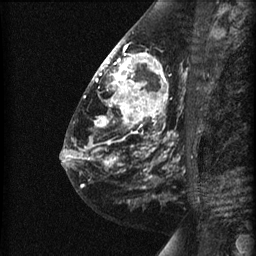
Breast MRI (dynamic contrast-enhanced), one sagittal slice. Slice 28 of 60 in the series (ordered by position). Dynamic contrast-enhanced series, image 2 of 3 at this slice position (ordered by acquisition). 1.5 T. TE 4.2 ms, TR 22.7 ms. 256 × 256 image matrix, field of view 180 × 180 mm. Patient: female, 48 years. From the clinical record (not read from this slice): setting: breast cancer imaged before/during neoadjuvant chemotherapy; receptor status: triple-negative.
Outlined on this slice (semi-automatic segmentation, software-assisted and operator-edited):
- analysis volume of interest (the breast-tissue region the enhancement analysis was run in; not a lesion): bounding box [x1, y1, x2, y2] px = [89, 27, 191, 180]
- tumour enhancement mask (voxels above the 90 % enhancement threshold inside the analysis volume of interest): [94, 44, 167, 160]